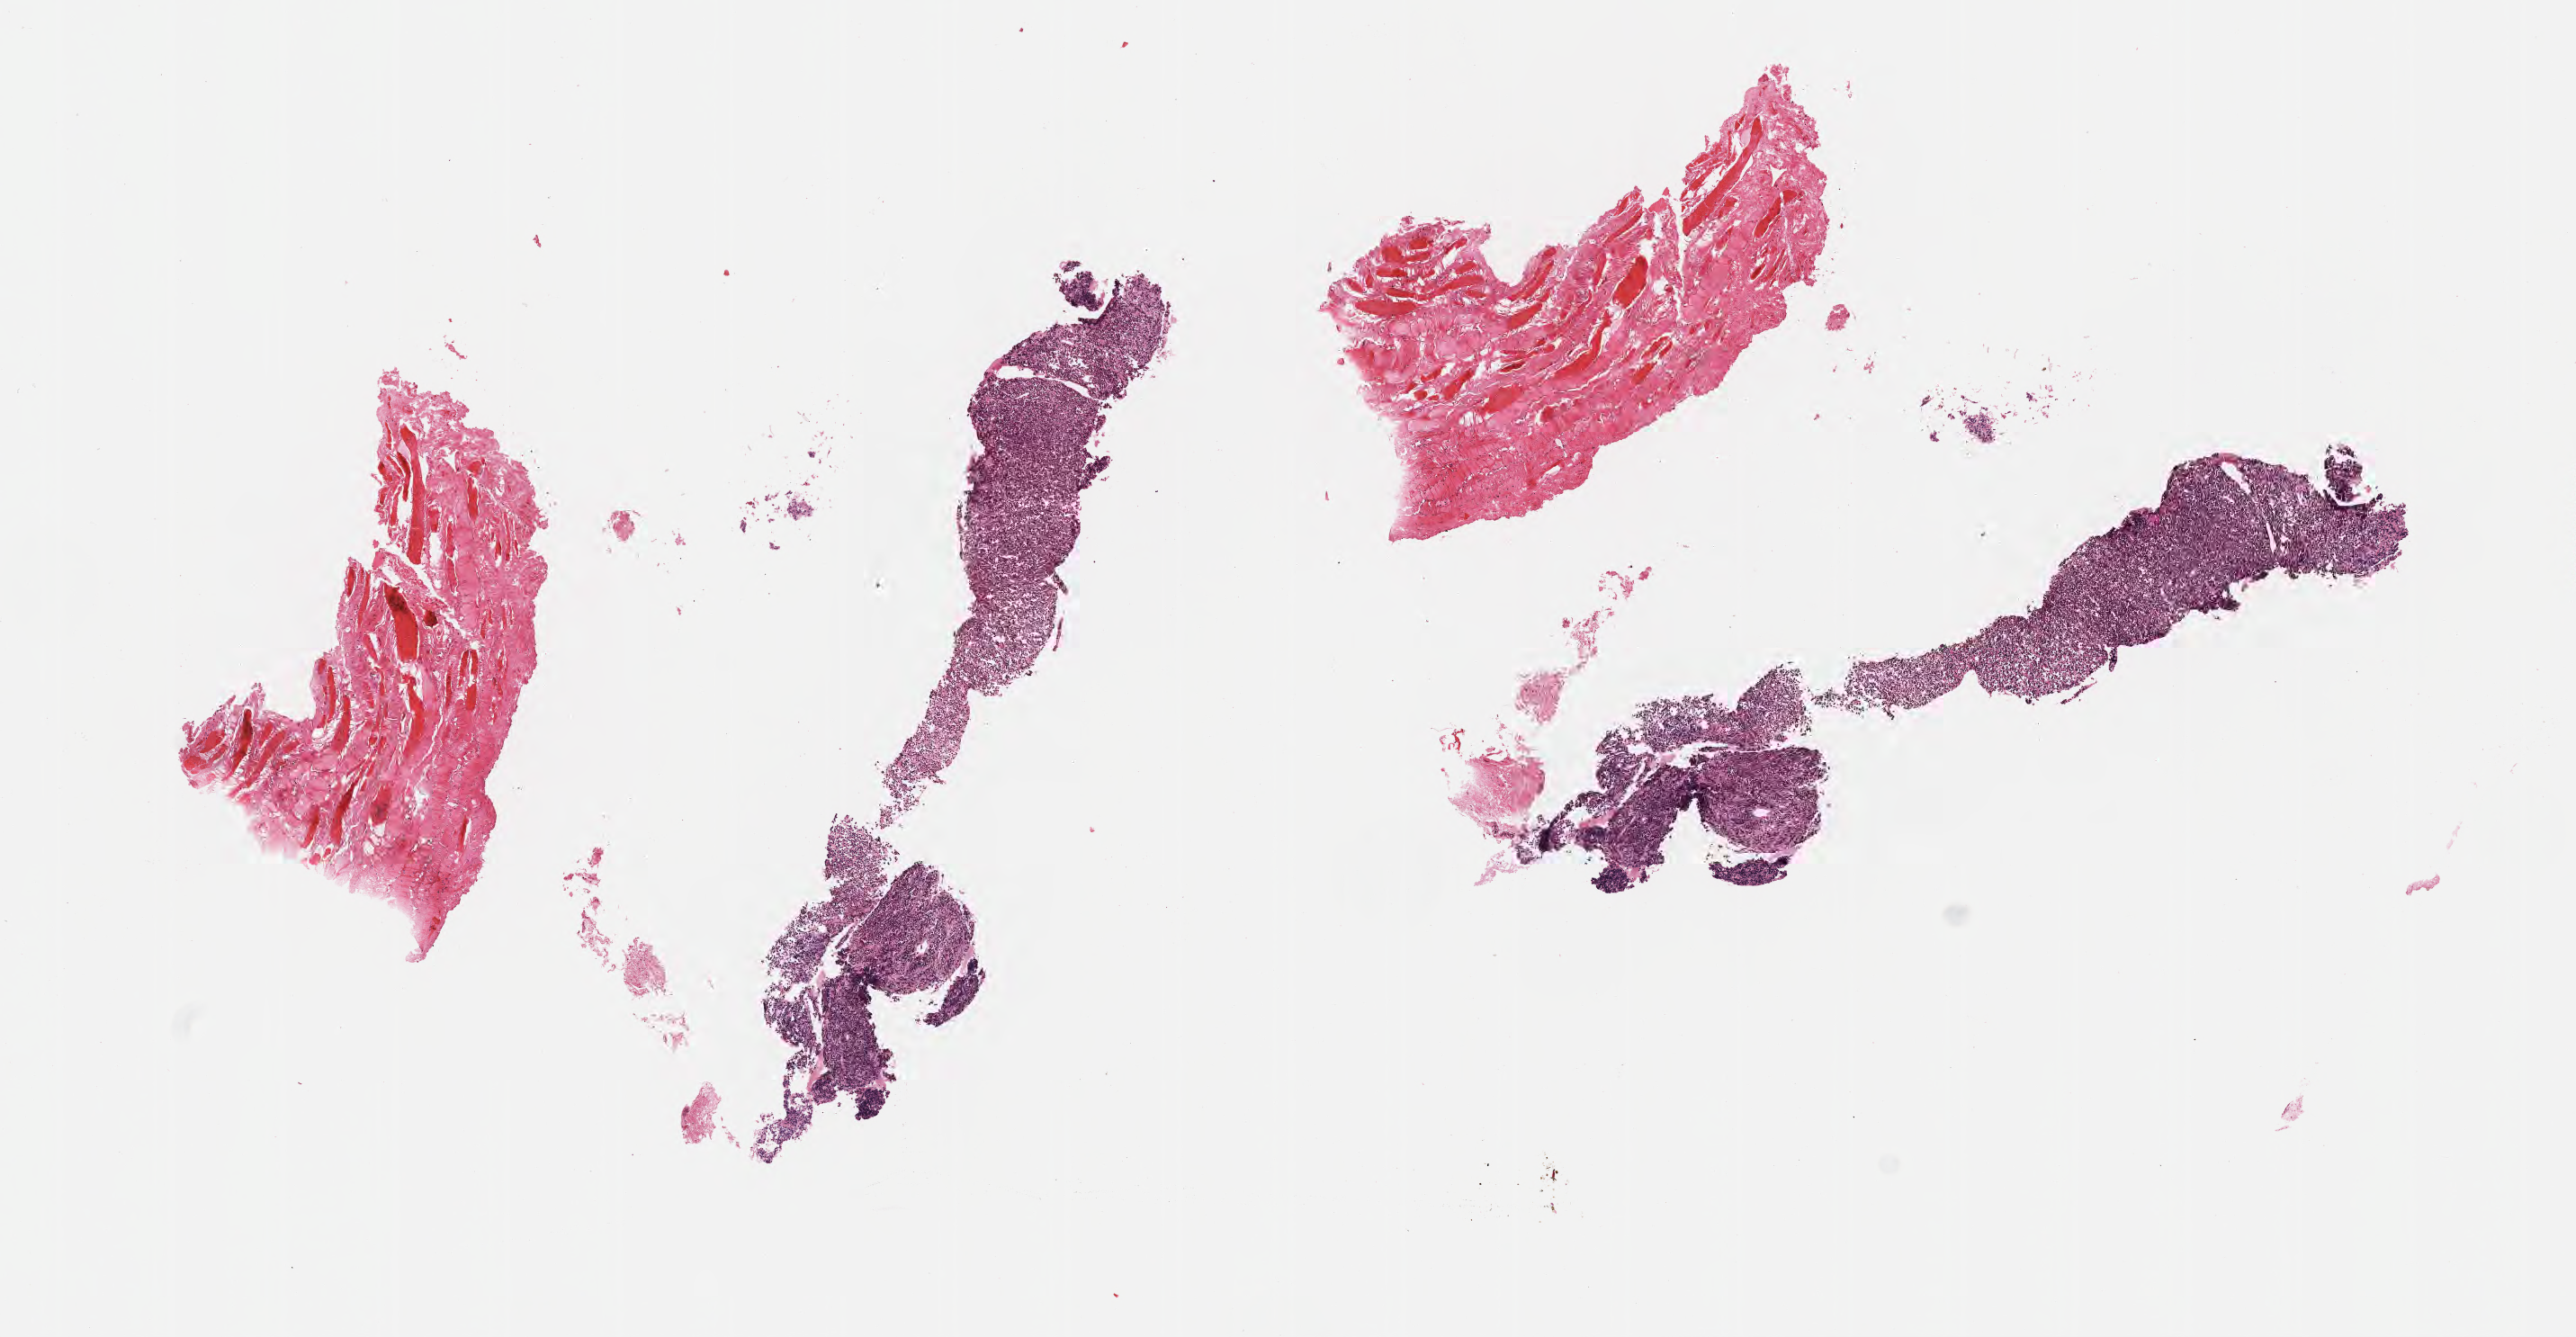
Digitized hematoxylin and eosin (H&E)-stained section — shown as a low-resolution overview of the whole scanned area (about 11.6 x 6.0 mm). Formalin-fixed paraffin-embedded section. Specimen: primary tumor. Anatomic site: liver. Patient sex: male. Composition of this section per pathologist review: tumor cells 45%, tumor nuclei 85%, stromal cells 50%, necrosis 5%, normal cells 0%. Inflammatory infiltration, as recorded: lymphocyte infiltration 20%, monocyte infiltration 30%, neutrophil infiltration 15%.
Section: bottom of the tissue portion. Diagnosis: Burkitt lymphoma, NOS.